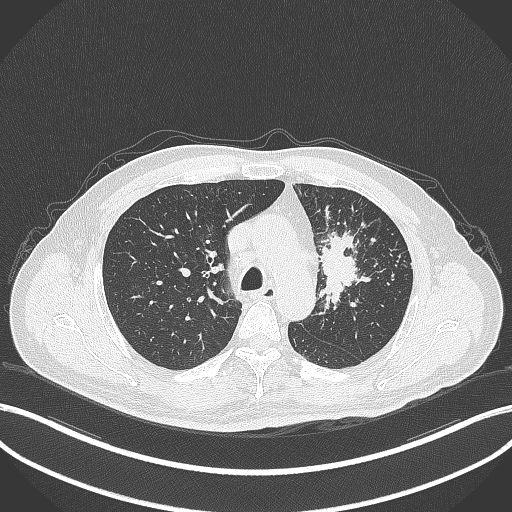
Chest CT, one axial slice; position 248 of 386 along the scan axis; lung window (W 1500 / L -600 HU); 1 mm slice thickness; 512 × 512 image matrix, field of view 400 × 400 mm. Patient: male, 69 years. Case-level facts recorded for this patient, not image findings: clinical TNM (as recorded): T2a N2 M0; histopathological grade: G2-3.
Outlined on this slice (rectangle marked by the reading radiologist):
- lung tumour (recorded histology: adenocarcinoma): bounding box [x1, y1, x2, y2] px = [315, 225, 373, 314]